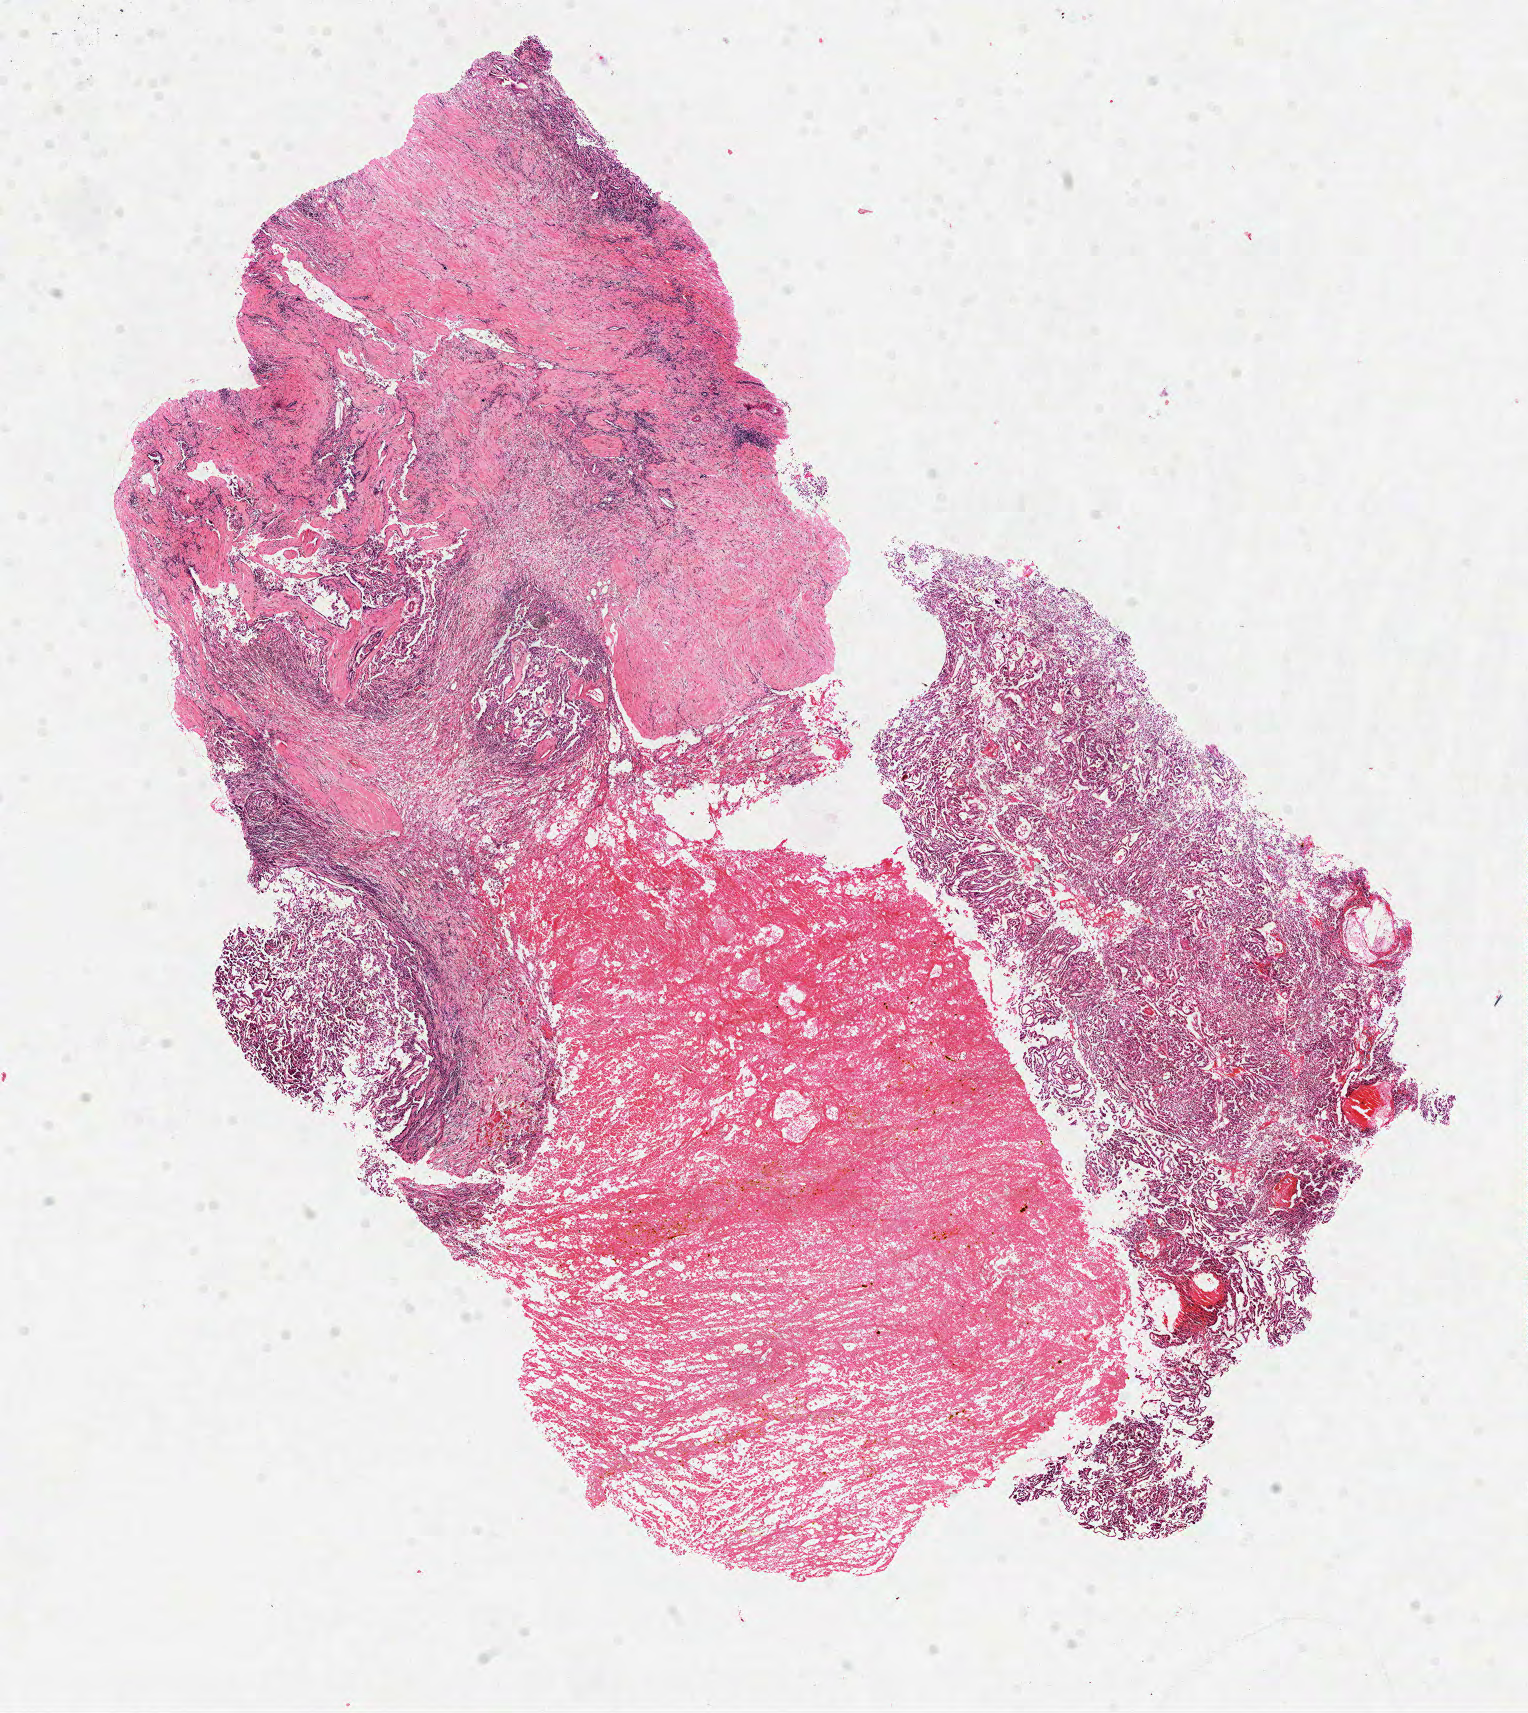
Whole-slide histology image, Hematoxylin and eosin (H&E) stained — whole scanned area (about 12.3 x 13.8 mm) shown as a low-resolution overview, formalin-fixed paraffin-embedded (FFPE) diagnostic section, primary tumour sample from the kidney. Patient: female, age at initial diagnosis 72 years.
AJCC pathologic stage: IV (6th edition). TNM: T3 N2 M0. Diagnosis: Papillary adenocarcinoma, NOS.